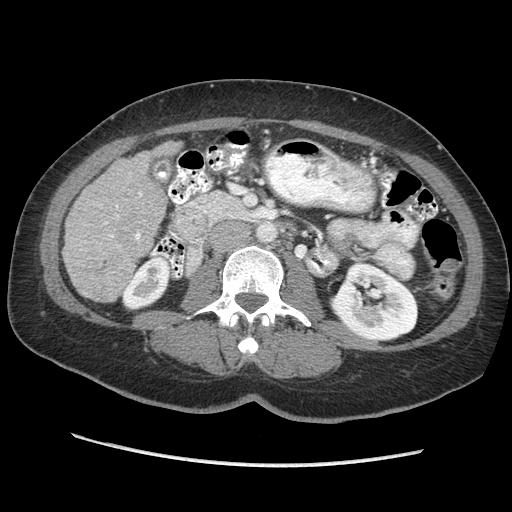
Contrast-enhanced abdominal CT (liver protocol), one axial slice; slice 101 of 170 in the series (ordered by position); reconstruction kernel STANDARD; 140 kVp; soft-tissue window (W 400 / L 40 HU); 2.5 mm slice thickness; 512 × 512 image matrix, field of view 360 × 360 mm. From the clinical record (not read from this slice): diagnosis: hepatocellular carcinoma (patient treated with transarterial chemoembolisation; whether this scan precedes or follows treatment is not stated here); TNM stage (as recorded): Stage-II; Child-Pugh class: A; tumour differentiation: no biopsy; tumour size: 4 cm.
Structures marked on this image (semi-automatic segmentation, software-assisted and operator-edited):
- liver parenchyma outside the tumour (the mass and vessels are separate outlines, so this box may not span the whole liver): bounding box <62,141,180,302> (left, top, right, bottom; pixels)
- liver vessels: <100,192,142,247>